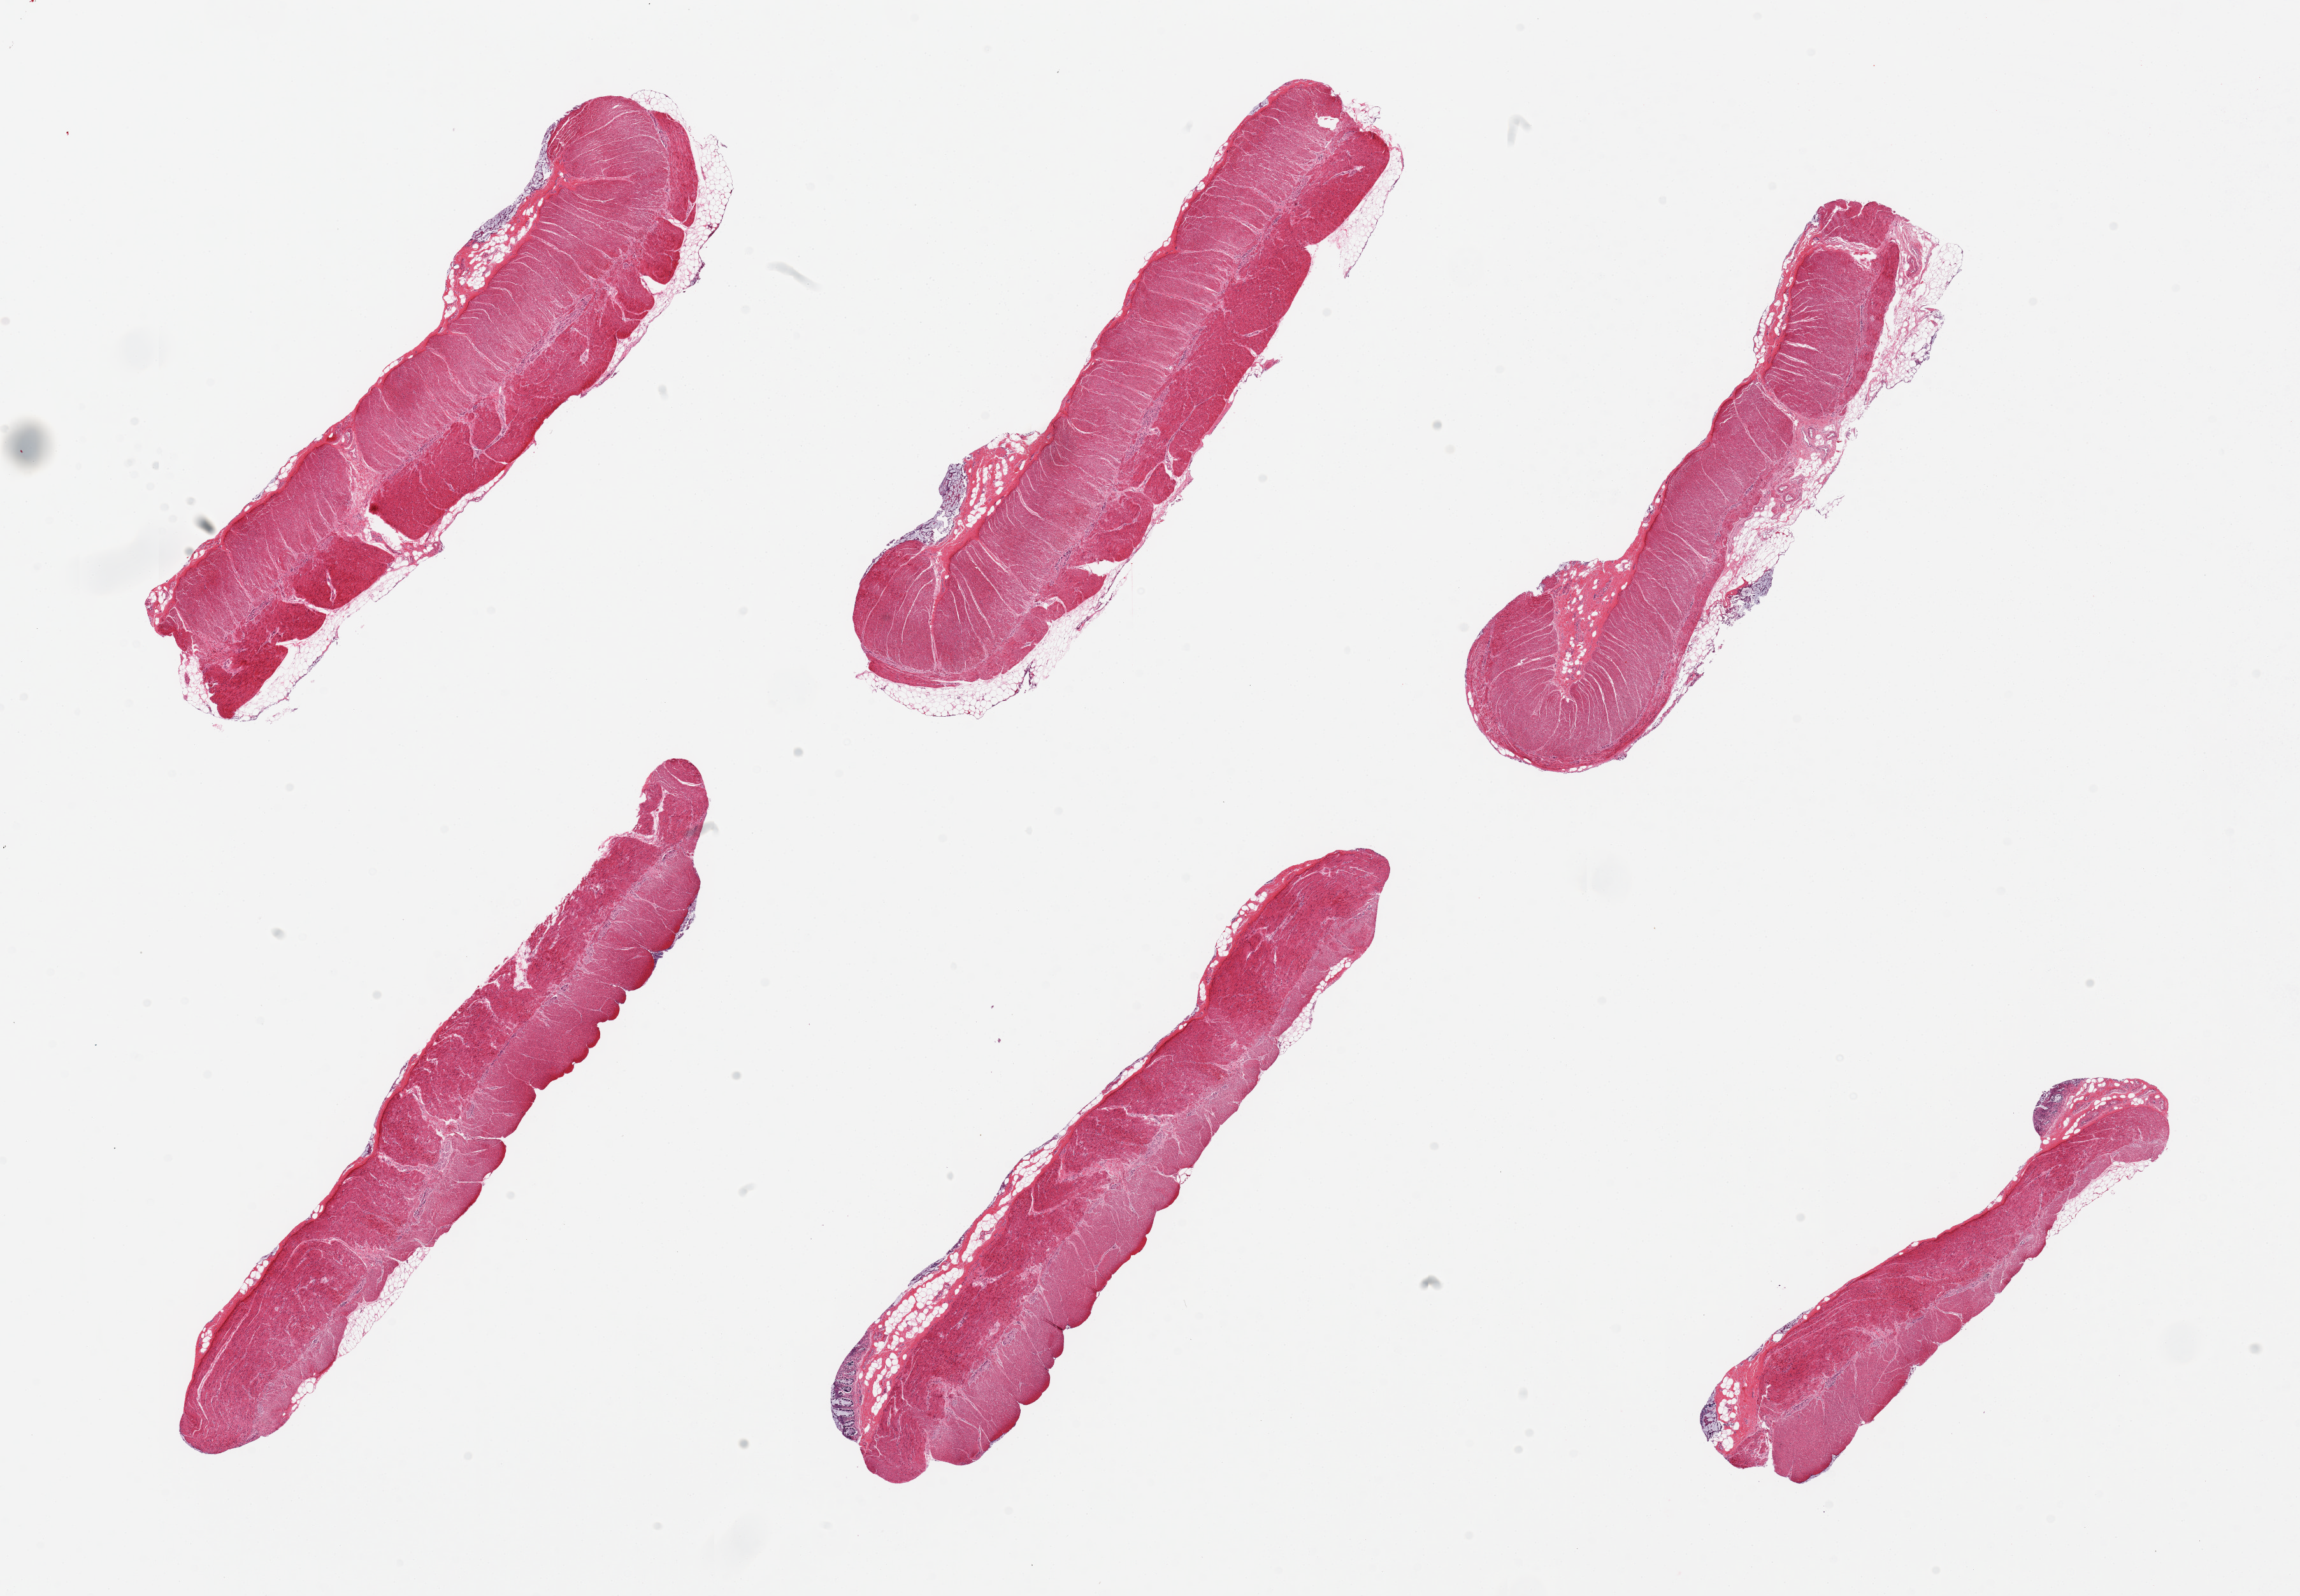
H&E whole-slide image — whole scanned area (about 28.5 x 19.8 mm) shown as a low-resolution overview; PAXgene-fixed paraffin-embedded (PFPE) section; sampled site (target tissue): sigmoid colon; donor tissue sample. Female donor.
Reviewer comment on this tissue sample: 6 pieces; well trimmed muscularis.